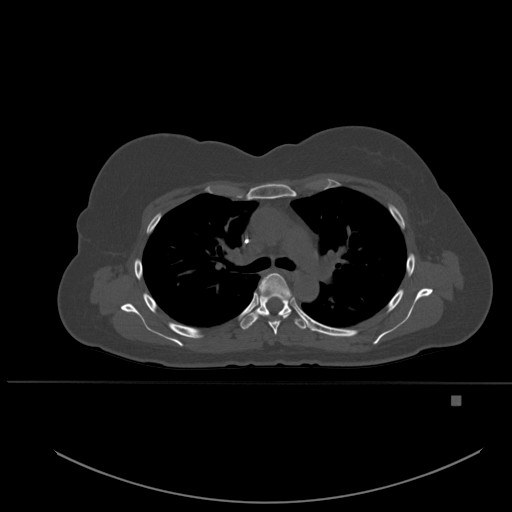
CT including the spine, one axial slice. Position 372 of 651 along the scan axis. Bone window (W 1800 / L 400 HU). 512 × 512 image matrix, field of view 443 × 443 mm. Female patient, age 49 years. Case-level facts recorded for this patient, not image findings: primary cancer: breast; vertebrae with lytic lesions (as recorded): L3, T12, L4.
Annotated regions visible in this slice (semi-automatic segmentation, software-assisted and operator-edited):
- T4 vertebra: bounding box [x1, y1, x2, y2] px = [259, 273, 292, 335]
- T5 vertebra: [240, 294, 307, 330]